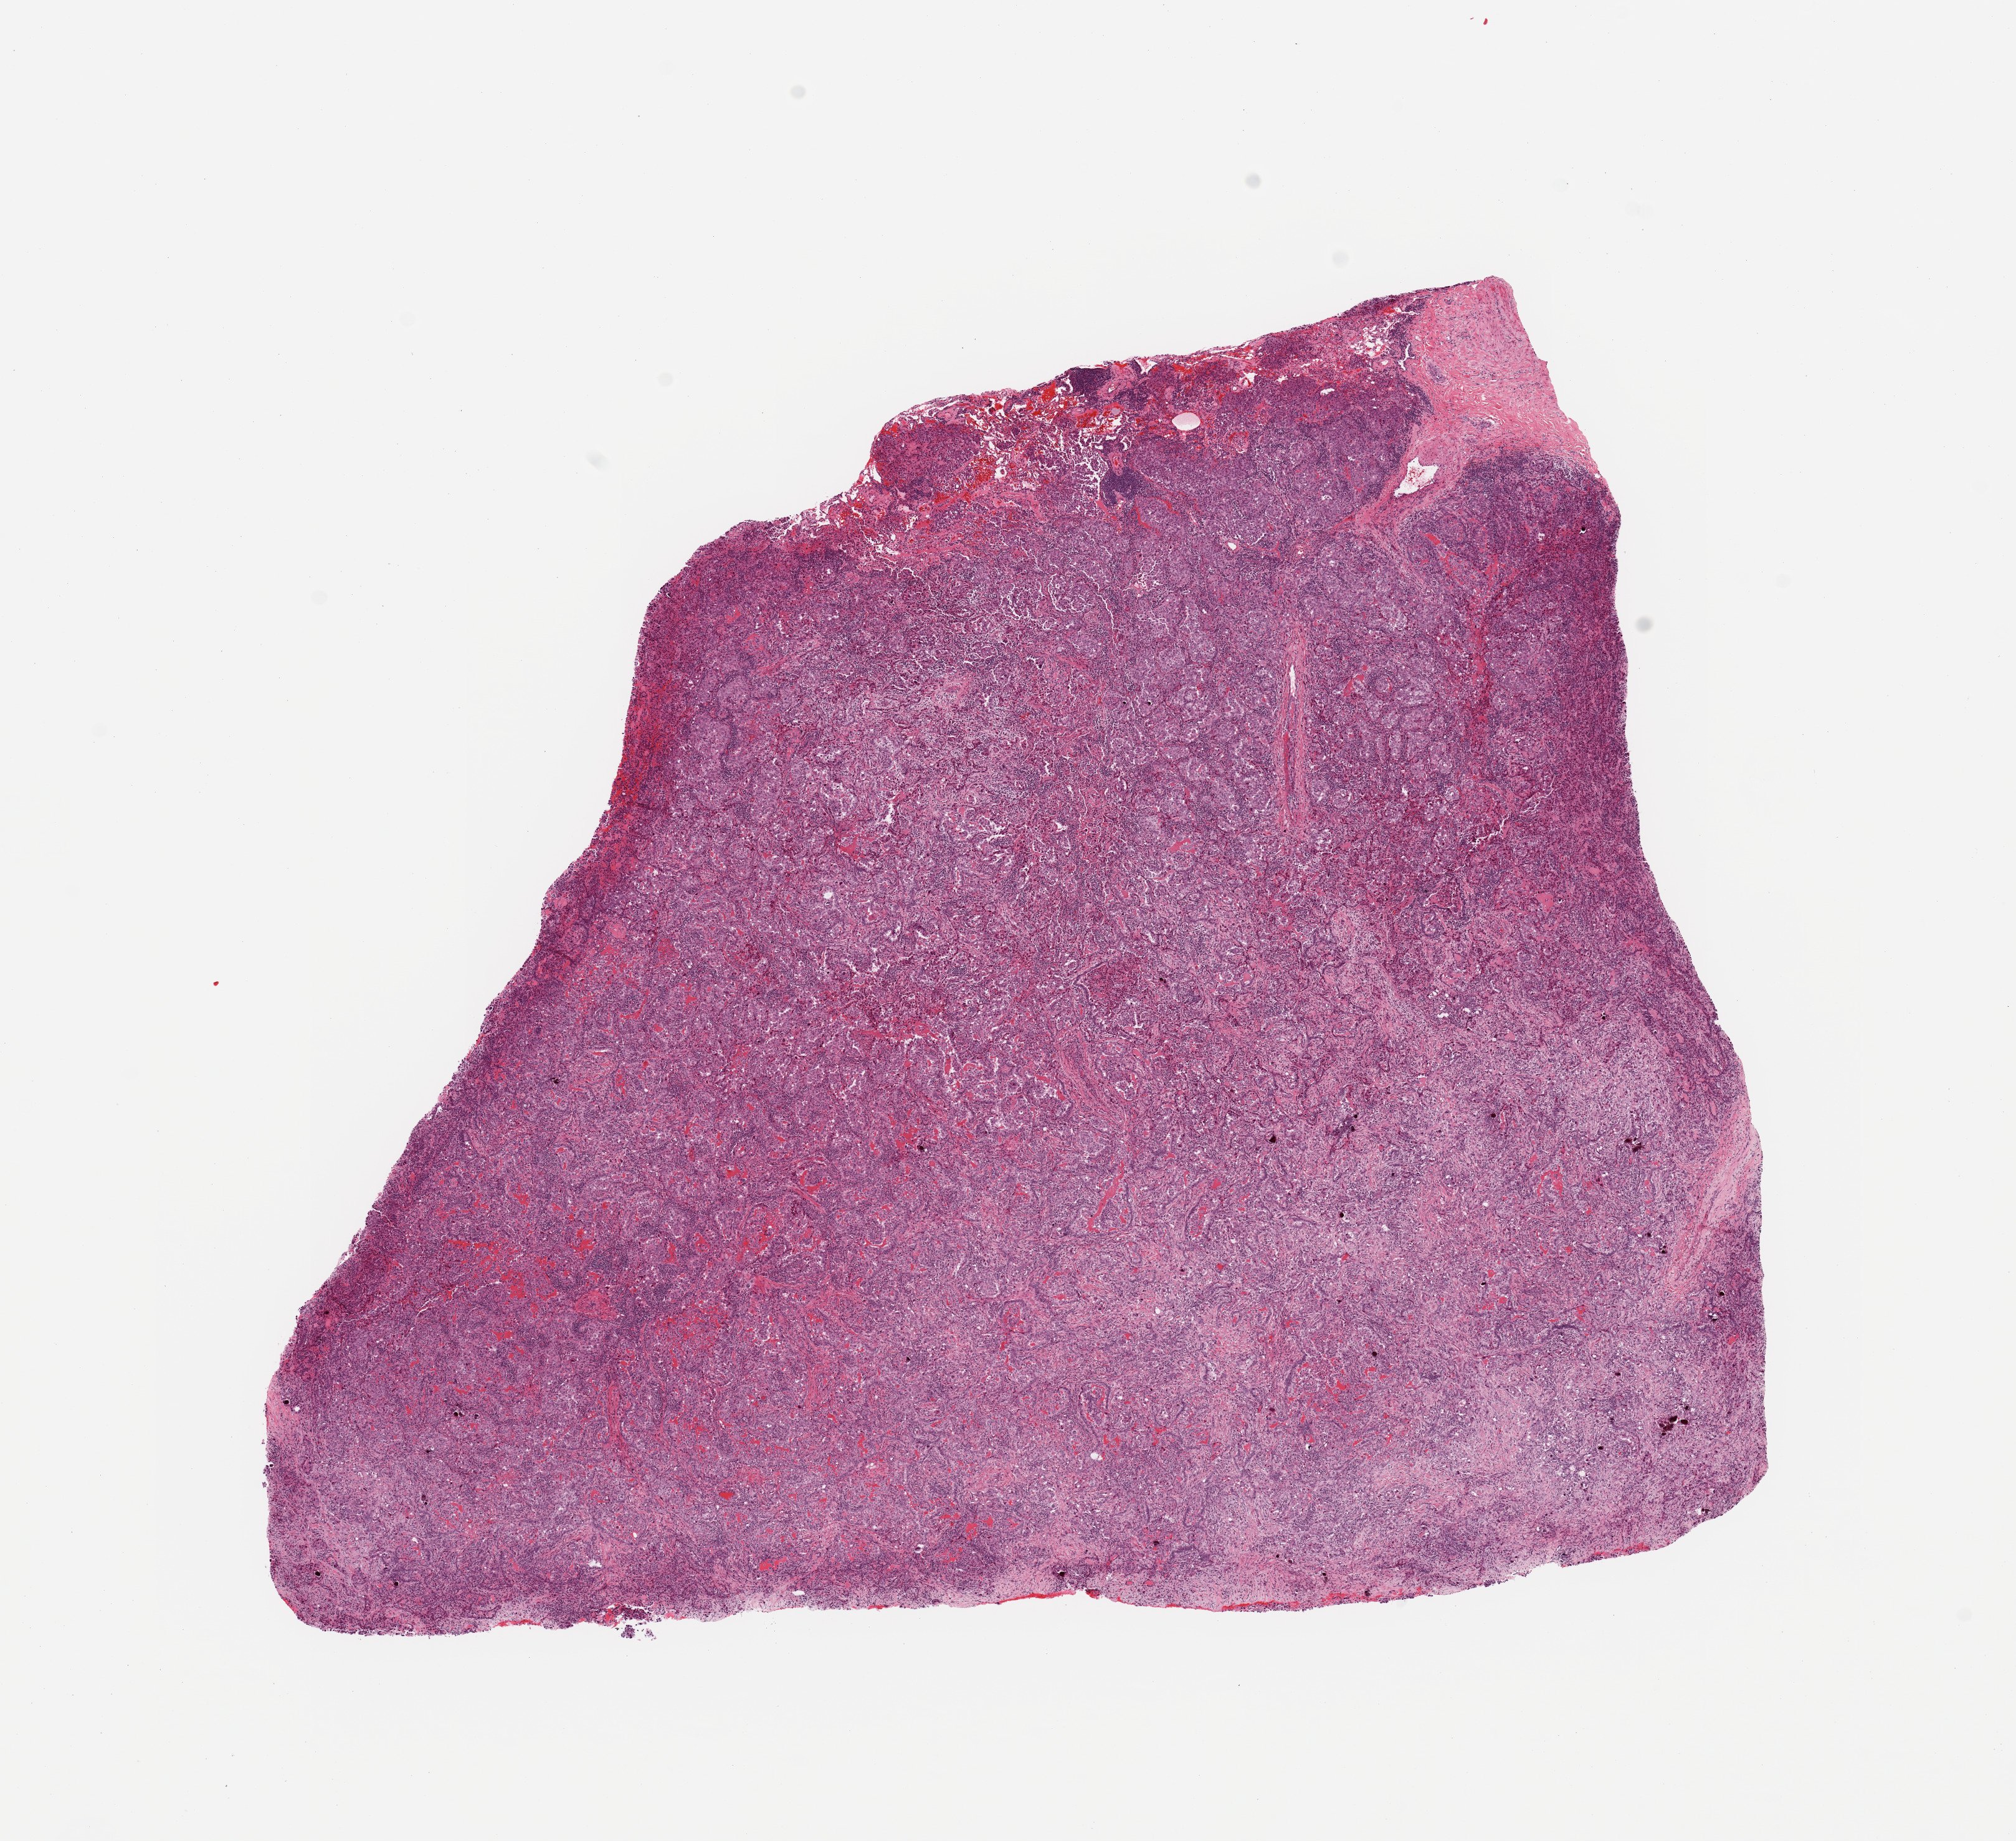
H&E-stained whole-slide image, a low-resolution overview of the entire scanned area, about 12.8 x 11.7 mm; tumour tissue sample, sampled site: lung. 61-year-old female patient. Histologic grade: G3 (poorly differentiated). Composition of this section per pathologist review: tumour nuclei 85%, necrosis 1%.
AJCC pathologic stage: IIA. Primary tumour site (as recorded): right upper lobe. Histologic diagnosis: Adenocarcinoma, NOS.